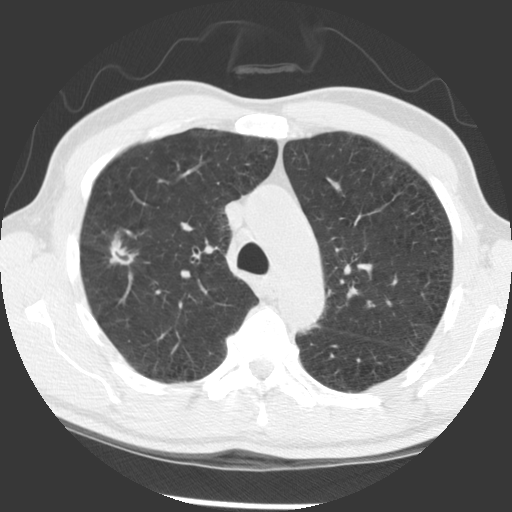
Axial slice from a low-dose chest CT screening exam. Baseline annual screen. Lung window (W 1500 / L -600 HU). 140 kVp. Slice 99 of 140 in the series. Male, age 56 years at enrolment. Current smoker at enrolment.
• Lesion marked by an expert reader, box from (x=71, y=229) to (x=140, y=285) px.
• Reader record for this screening exam (exam-level; its link to the box is not recorded): non-calcified nodule or mass ≥4 mm, right upper lobe, 12 × 7 mm, spiculated (stellate) margins, soft tissue attenuation.
• Official screen result: positive, change unspecified: nodule(s) >= 4 mm or enlarging nodule(s), mass(es), or other non-specific abnormalities suspicious for lung cancer.